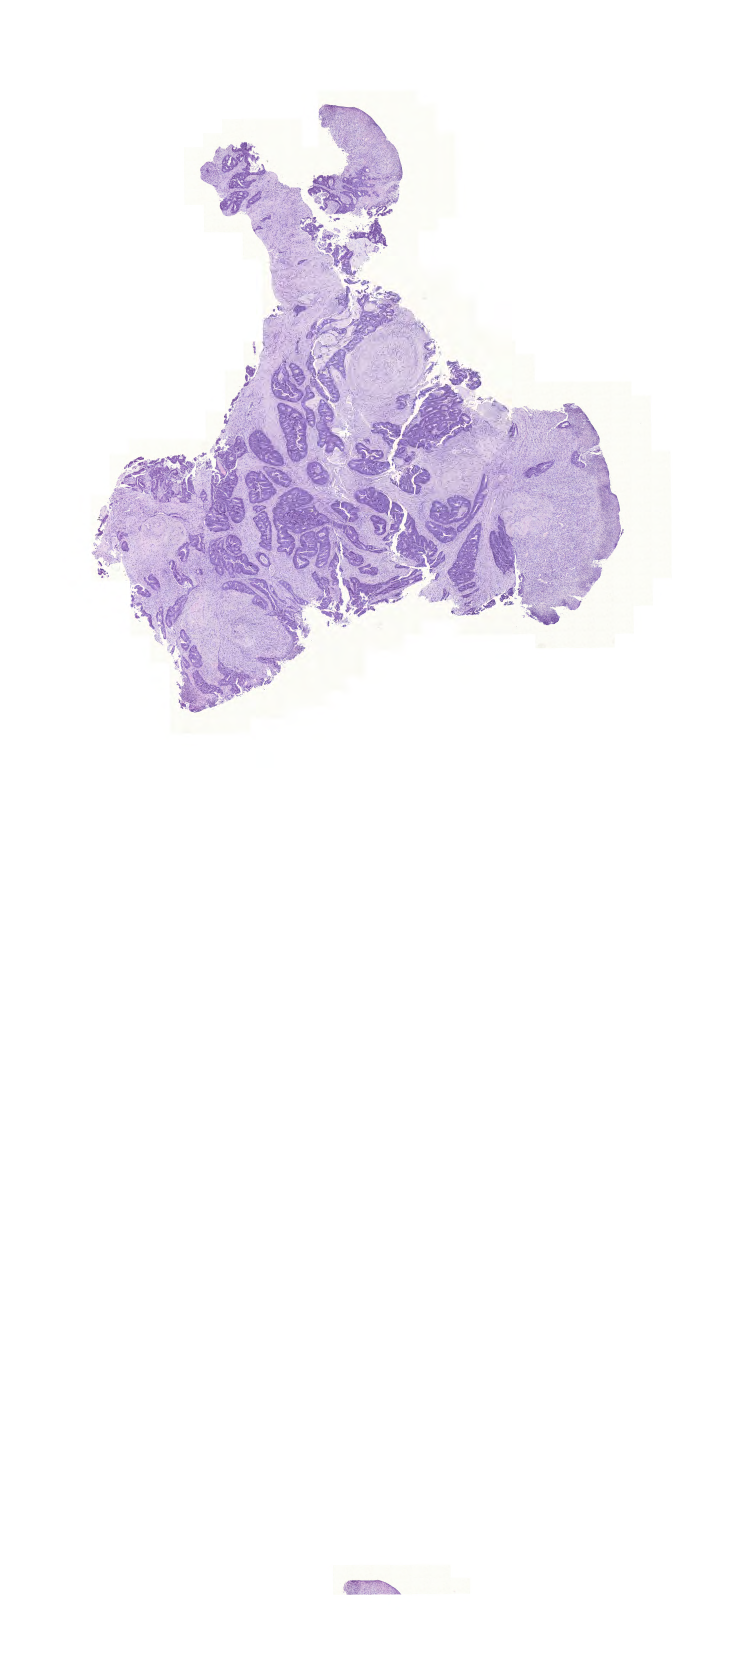
H&E whole-slide image — whole scanned area (about 11.1 x 24.9 mm, from a 20x scan) shown as a low-resolution overview. FFPE section. Primary tumour sample from the colon. Female patient.
Lymph nodes positive (case pathology): 0 of 15 examined. AJCC pathologic stage: IIA. Pathologic diagnosis: Adenocarcinoma, NOS.